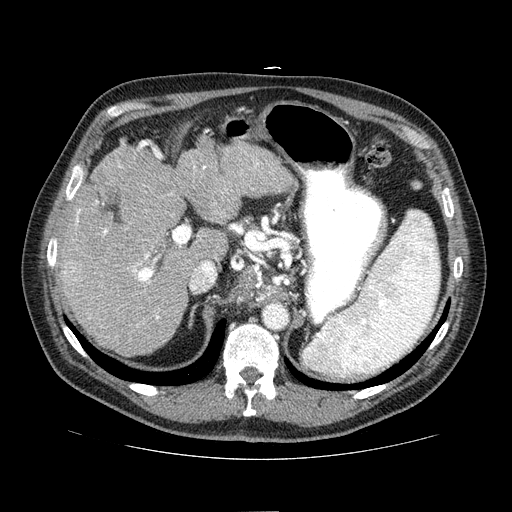
Contrast-enhanced abdominal CT (liver protocol), one axial slice. Position 47 of 81 along the scan axis. Reconstruction kernel STANDARD. One of 2 acquisitions stored at this slice position. Soft-tissue window (W 400 / L 40 HU). 512 × 512 image matrix. From the clinical record (not read from this slice): diagnosis: hepatocellular carcinoma (patient treated with transarterial chemoembolisation; whether this scan precedes or follows treatment is not stated here); TNM stage (as recorded): Stage-IIIA; Child-Pugh class: A; tumour differentiation: well differentiated; tumour nodularity: multinodular.
Outlined on this slice (semi-automatically segmented with operator editing):
- liver parenchyma outside the tumour (the mass and vessels are separate outlines, so this box may not span the whole liver): bounding box <58,136,294,356> (left, top, right, bottom; pixels)
- liver vessels: <64,155,259,326>